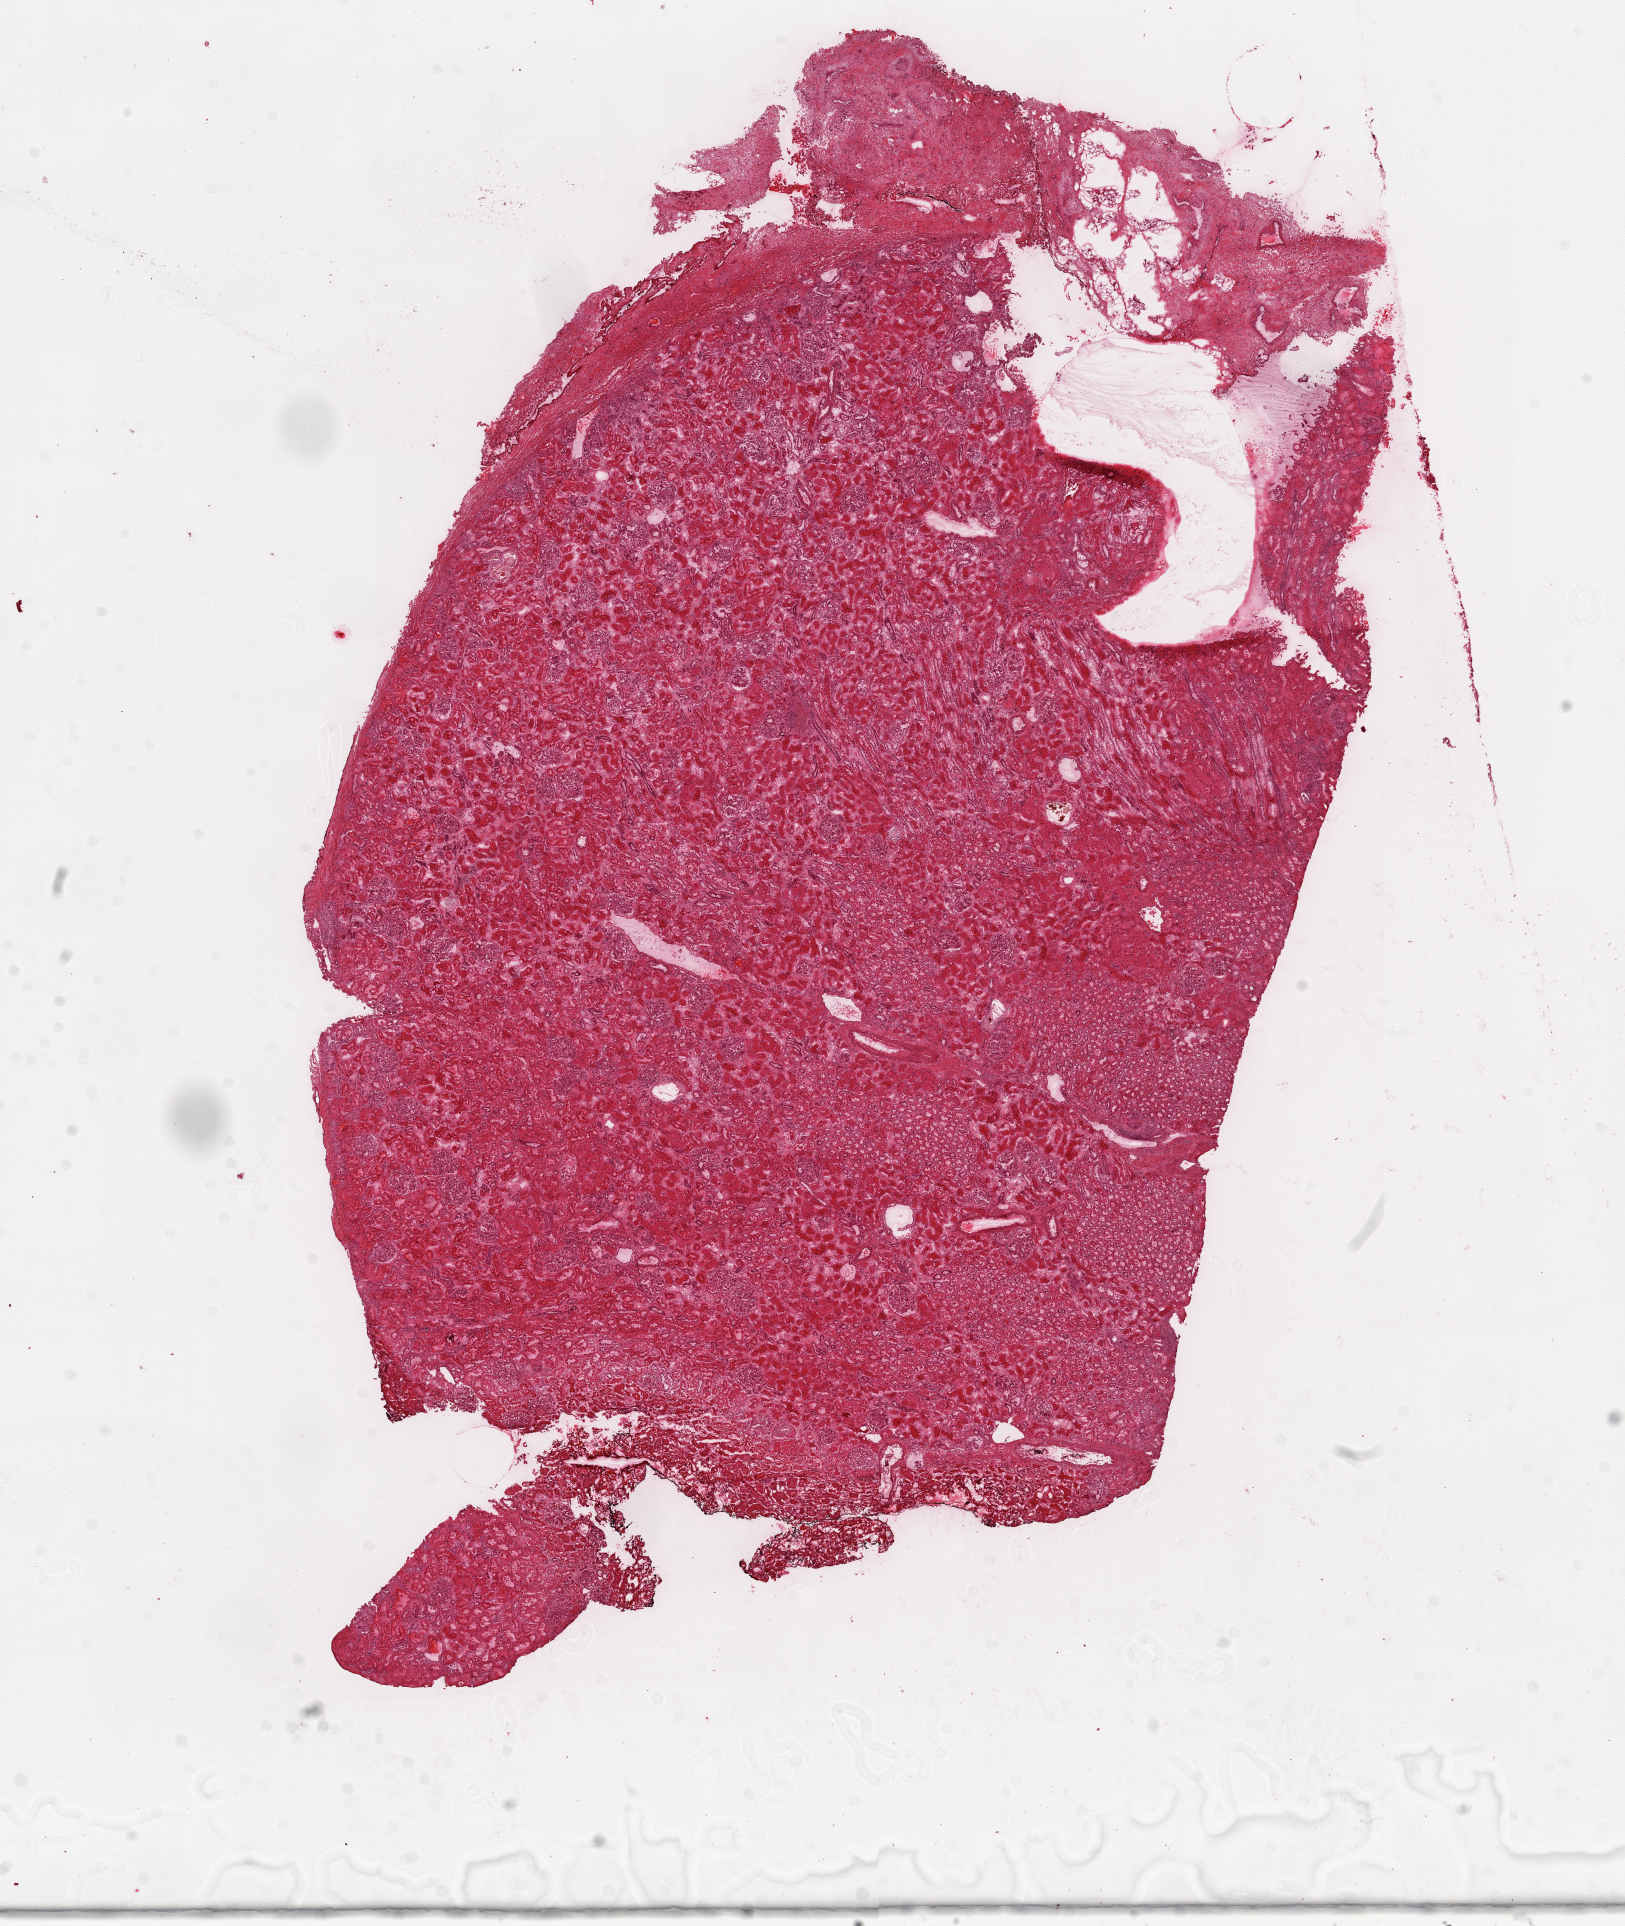
H&E whole-slide image, a low-resolution overview of the entire scanned area, about 13.0 x 15.5 mm, frozen section from the top of the tissue portion, sample: solid tissue normal (non-tumour tissue), kidney. Female, age 43 years at initial diagnosis.
This section: solid tissue normal sample (biorepository sample class). Patient diagnosis: Clear cell adenocarcinoma, NOS.